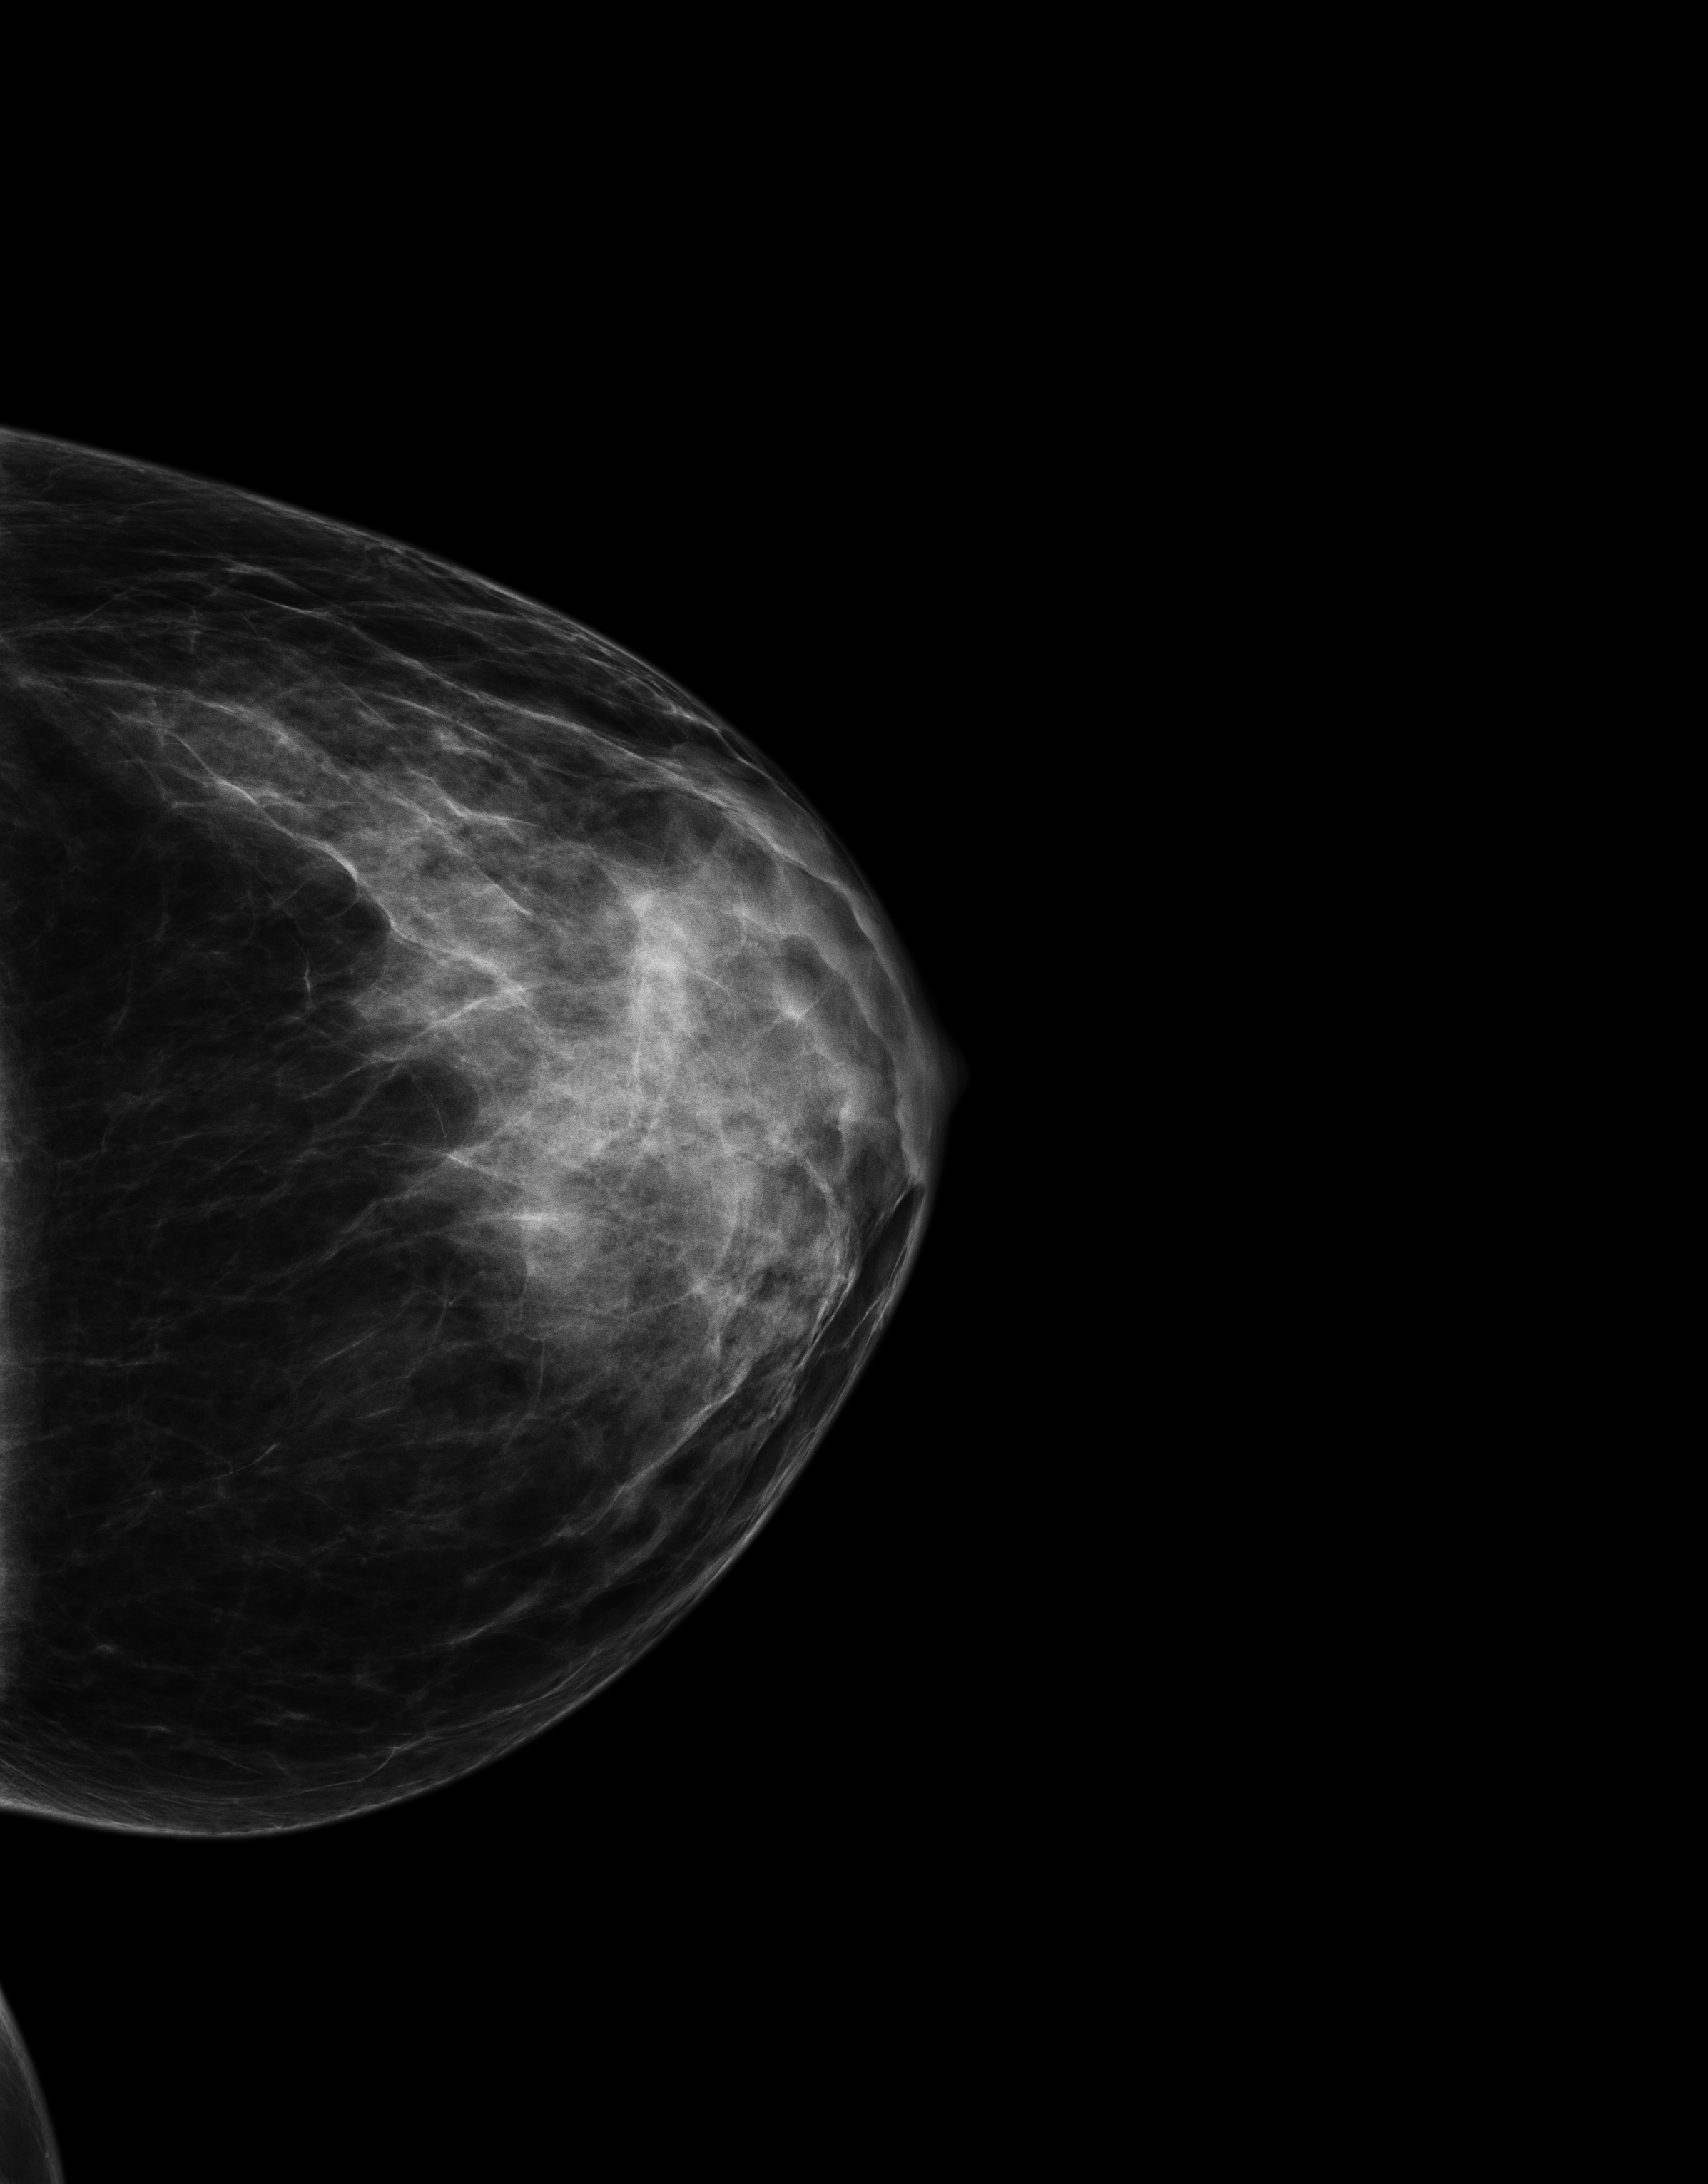
Screening examination, compressed breast thickness 44 mm. Patient aged 49 years (female).
Image type: full-field digital mammogram. Breast: left. Projection: cranio-caudal projection.